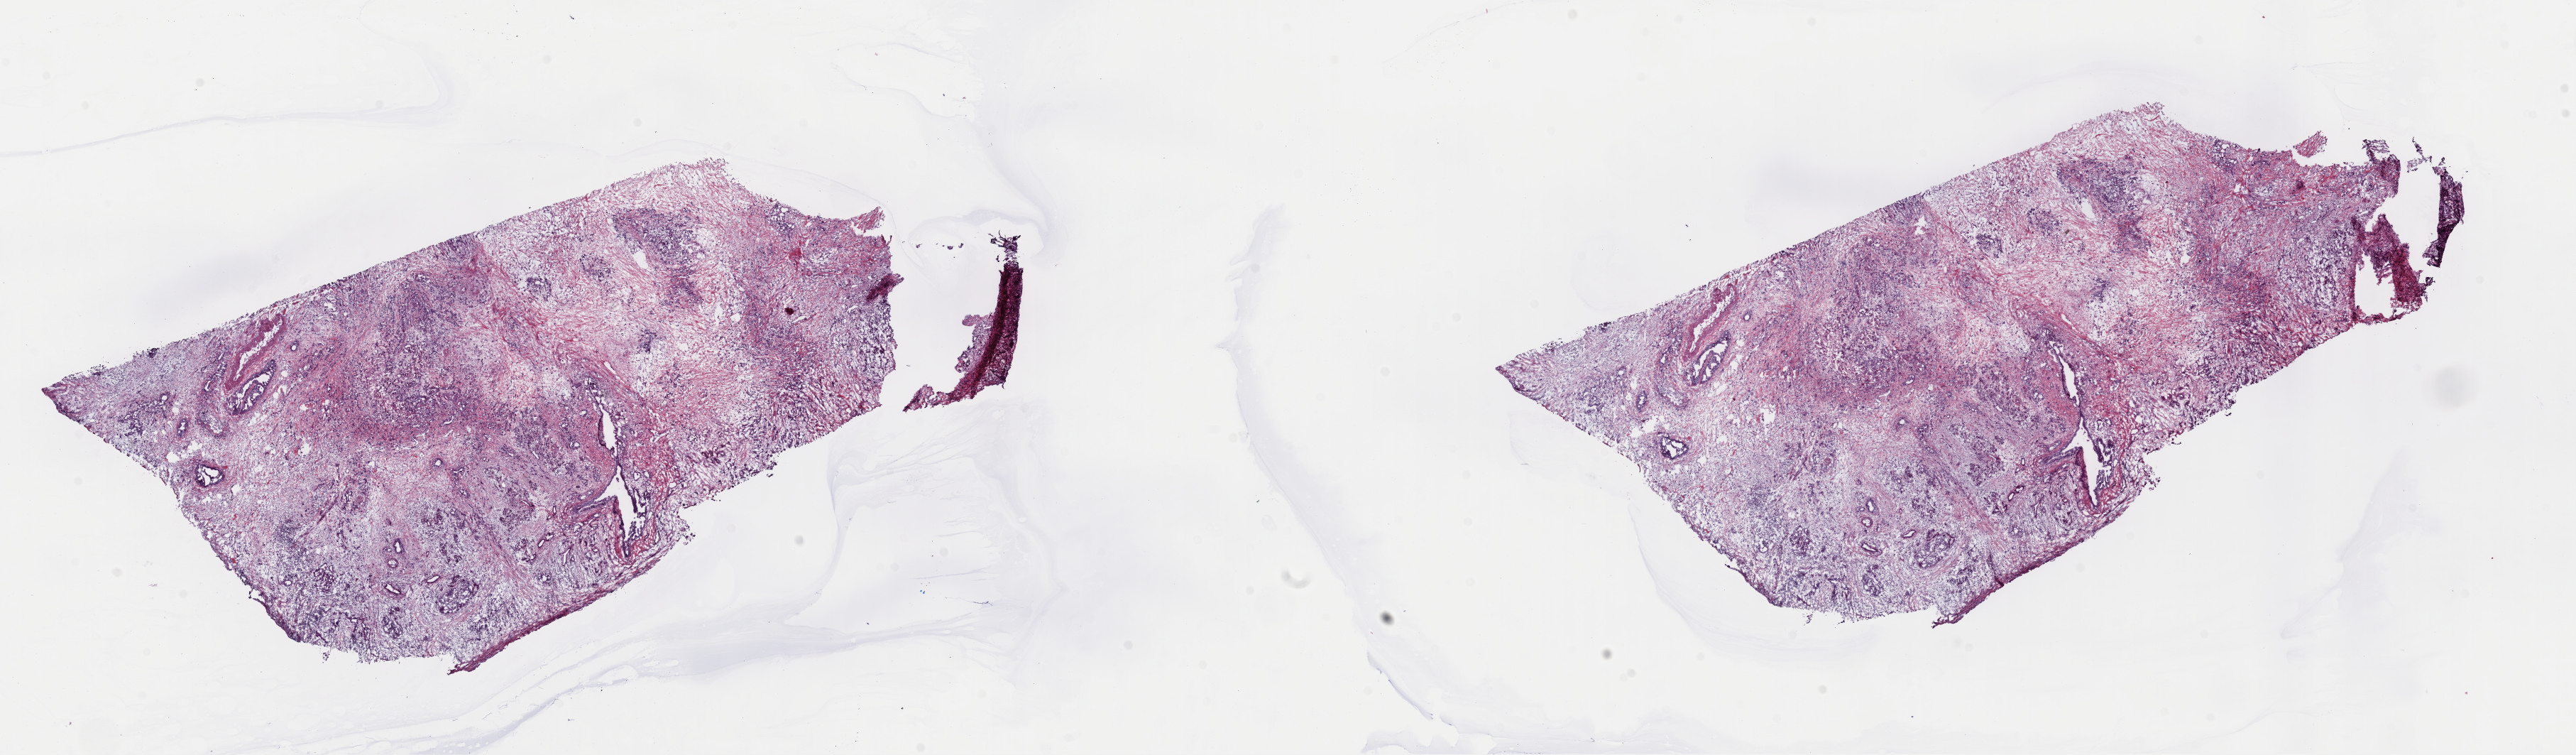
H&E whole-slide image — shown as a low-resolution overview of the whole scanned area (about 28.7 x 8.4 mm). Frozen section. Sample: primary tumour, pancreas. Female, age 72 years at initial diagnosis. Histologic grade: G2 (moderately differentiated). Composition of this section per pathologist review: tumour cells 35%, tumour nuclei 100%, normal cells 0%, stromal cells 65%, necrosis 0%. Inflammatory infiltration, as recorded: lymphocyte infiltration 6%, monocyte infiltration 10%, neutrophil infiltration 0%.
• diagnosis: Infiltrating duct carcinoma, NOS (body of pancreas)
• lymph nodes positive (case pathology): 4 of 28 examined
• AJCC pathologic stage: IIB (7th edition)